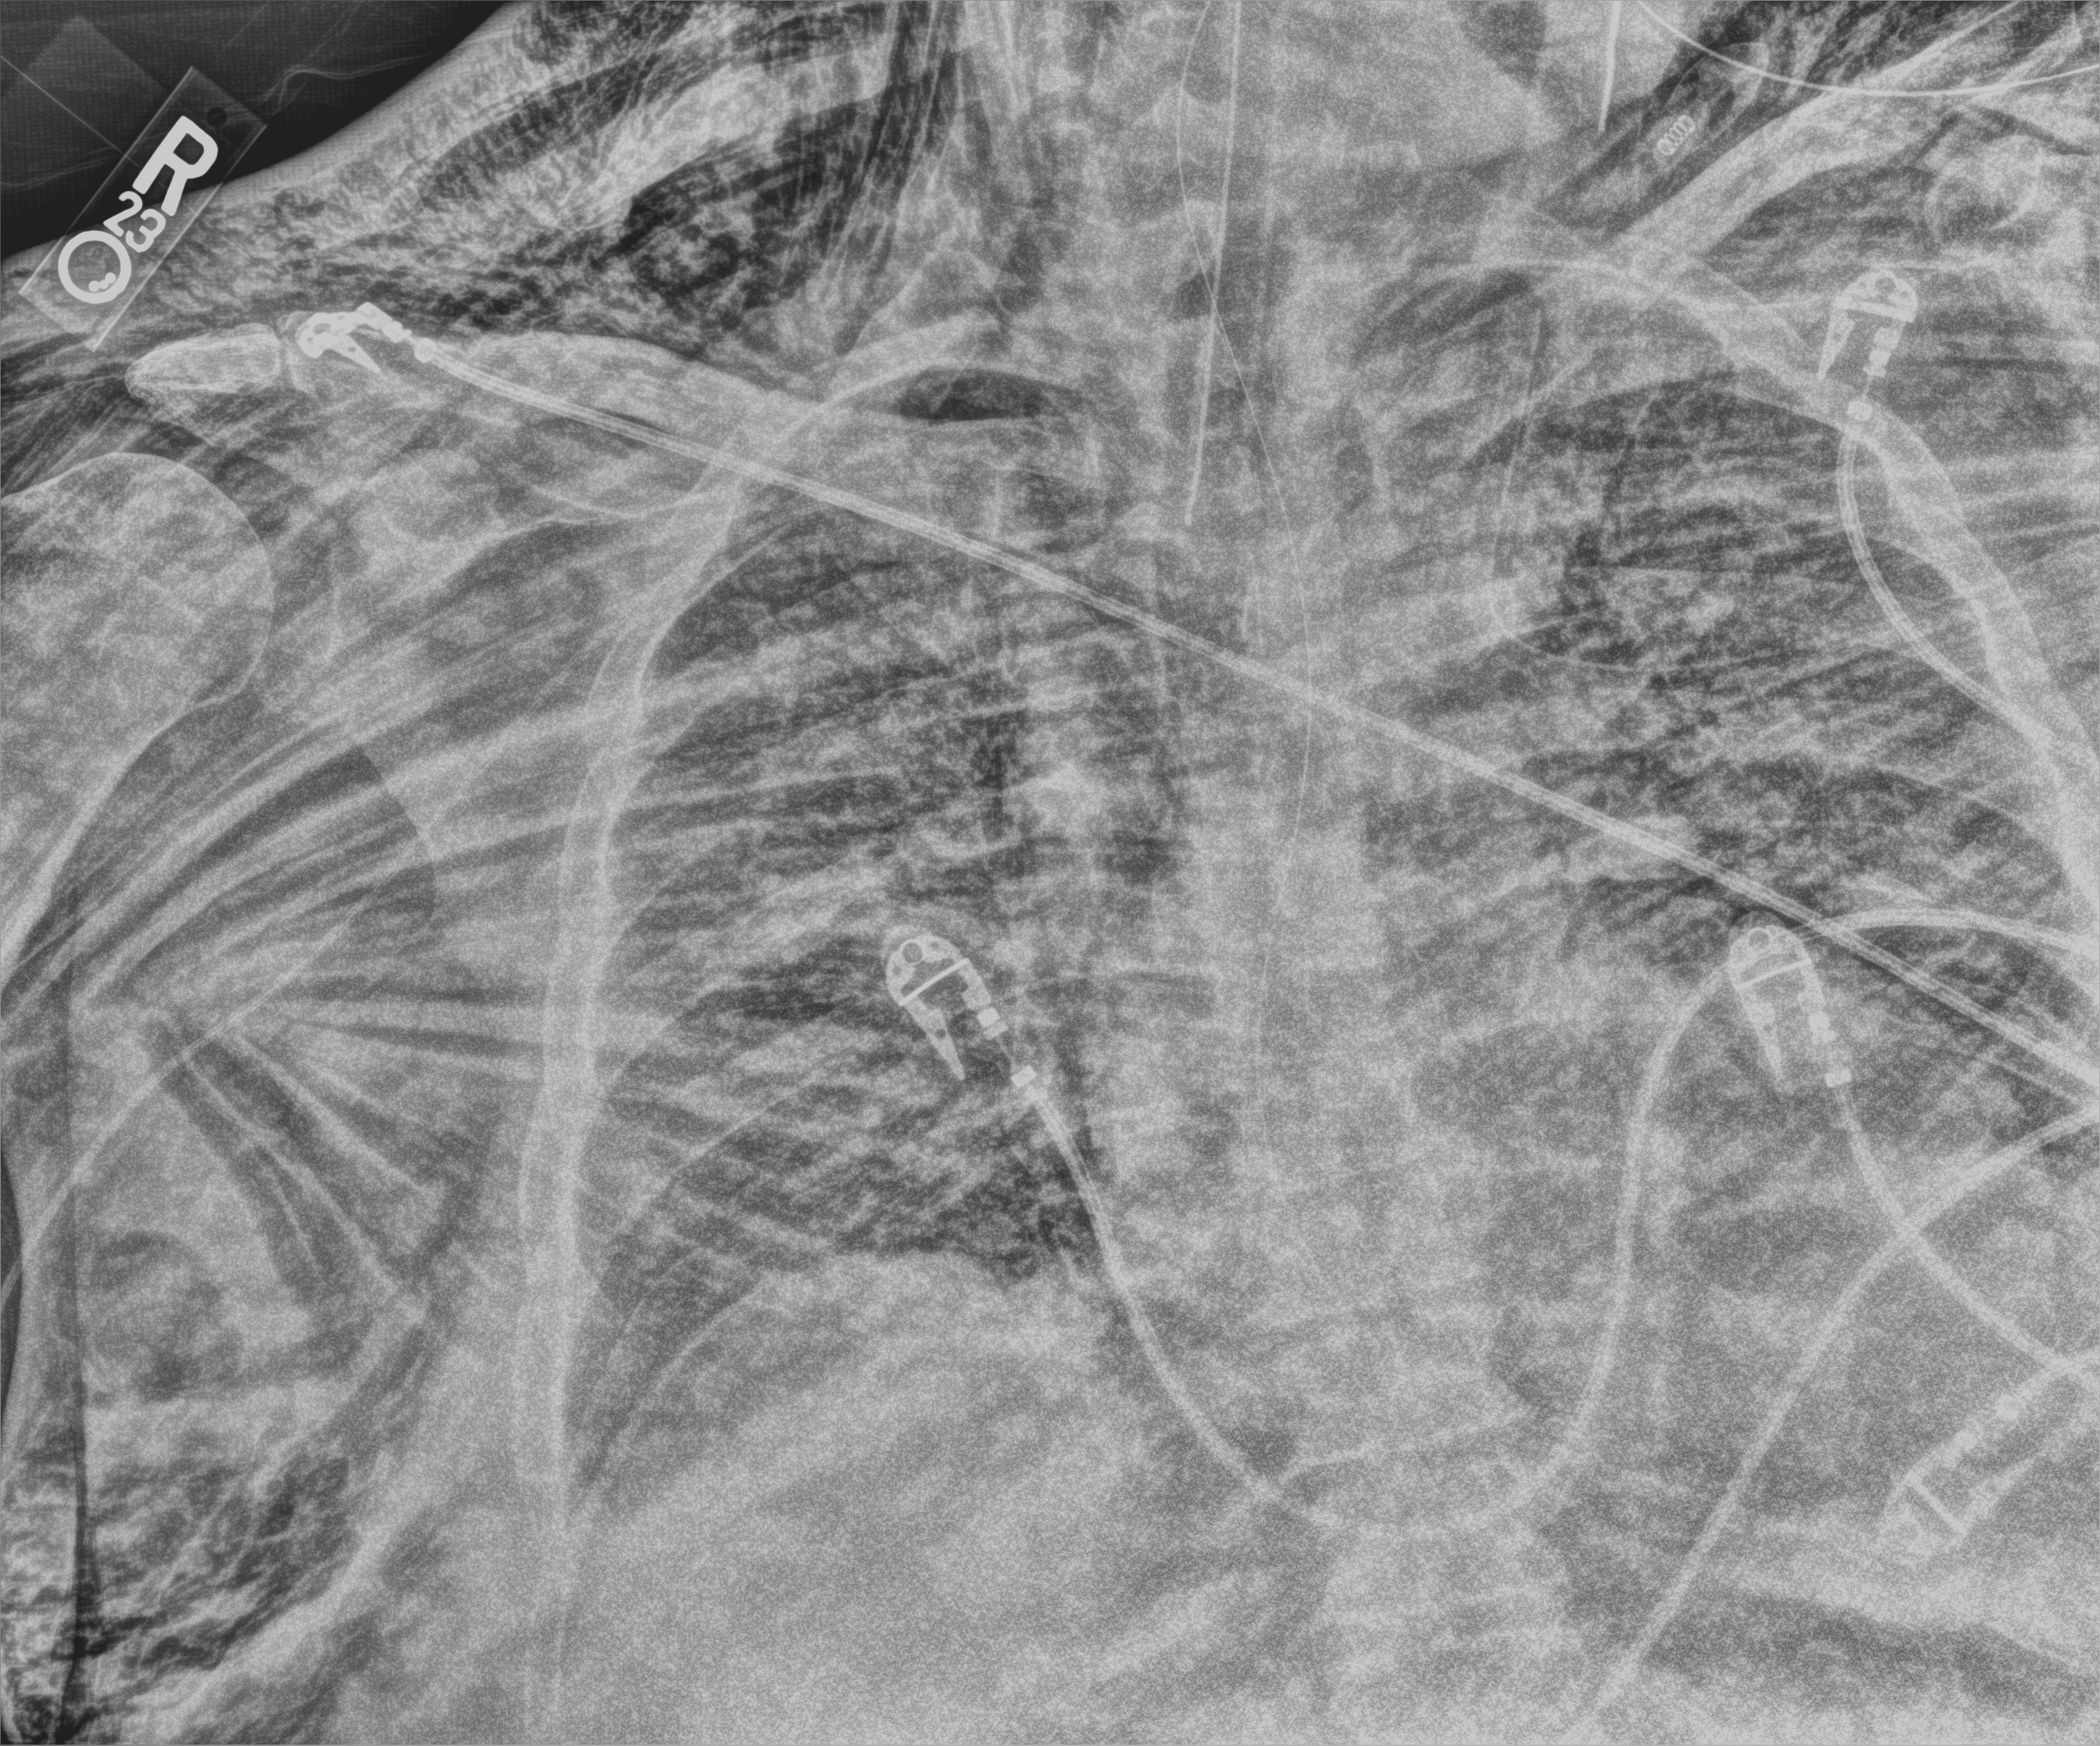
Portable chest radiograph; anteroposterior (AP) projection. Patient hospitalised with COVID-19, aged 18–59 years.
Admission-level facts for this patient (not findings on this image; timing relative to this image not recorded): other chronic lung disease (admission record): no; COPD (admission record): no; mechanically ventilated during this hospital stay: yes.